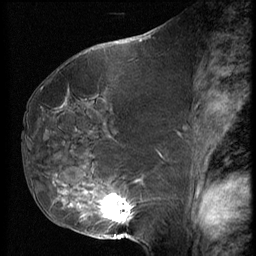
Breast MRI (dynamic contrast-enhanced), one sagittal slice; slice 33 of 62 in the series (ordered by position); 3 images stored at this slice position (order not interpretable as contrast timing); 1.5 T; TE 4.2 ms, TR 9 ms; 2.5 mm slice thickness; 256 × 256 image matrix, field of view 180 × 180 mm. Patient: female, 50 years. Case-level facts recorded for this patient, not image findings: setting: breast cancer imaged before/during neoadjuvant chemotherapy; receptor status: HR-positive, HER2-negative.
Outlined on this slice (semi-automatic segmentation, software-assisted and operator-edited):
- analysis volume of interest (the breast-tissue region the enhancement analysis was run in; not a lesion): bounding box <59,125,139,238> (left, top, right, bottom; pixels)
- tumour enhancement mask (voxels above the 140 % enhancement threshold inside the analysis volume of interest): <72,194,133,221>